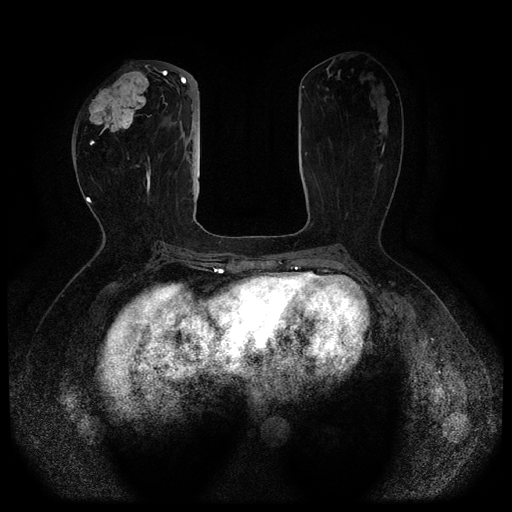
Breast MRI (dynamic contrast-enhanced, multi-phase), one axial slice; dynamic contrast-enhanced series, time point 2 of 5 at this slice position (early post-contrast); 1.5 T; TE 2.6 ms, TR 5.3 ms; 512 × 512 image matrix, field of view 350 × 350 mm. Female patient, age 51 years.
Outlined on this slice (semi-automatic segmentation, software-assisted and operator-edited):
- breast lesion (labelled 'tumour' in the annotation; benign lesions carry a separate 'benign' label): bounding box (x1, y1, x2, y2) in pixels: (84, 69, 150, 146)